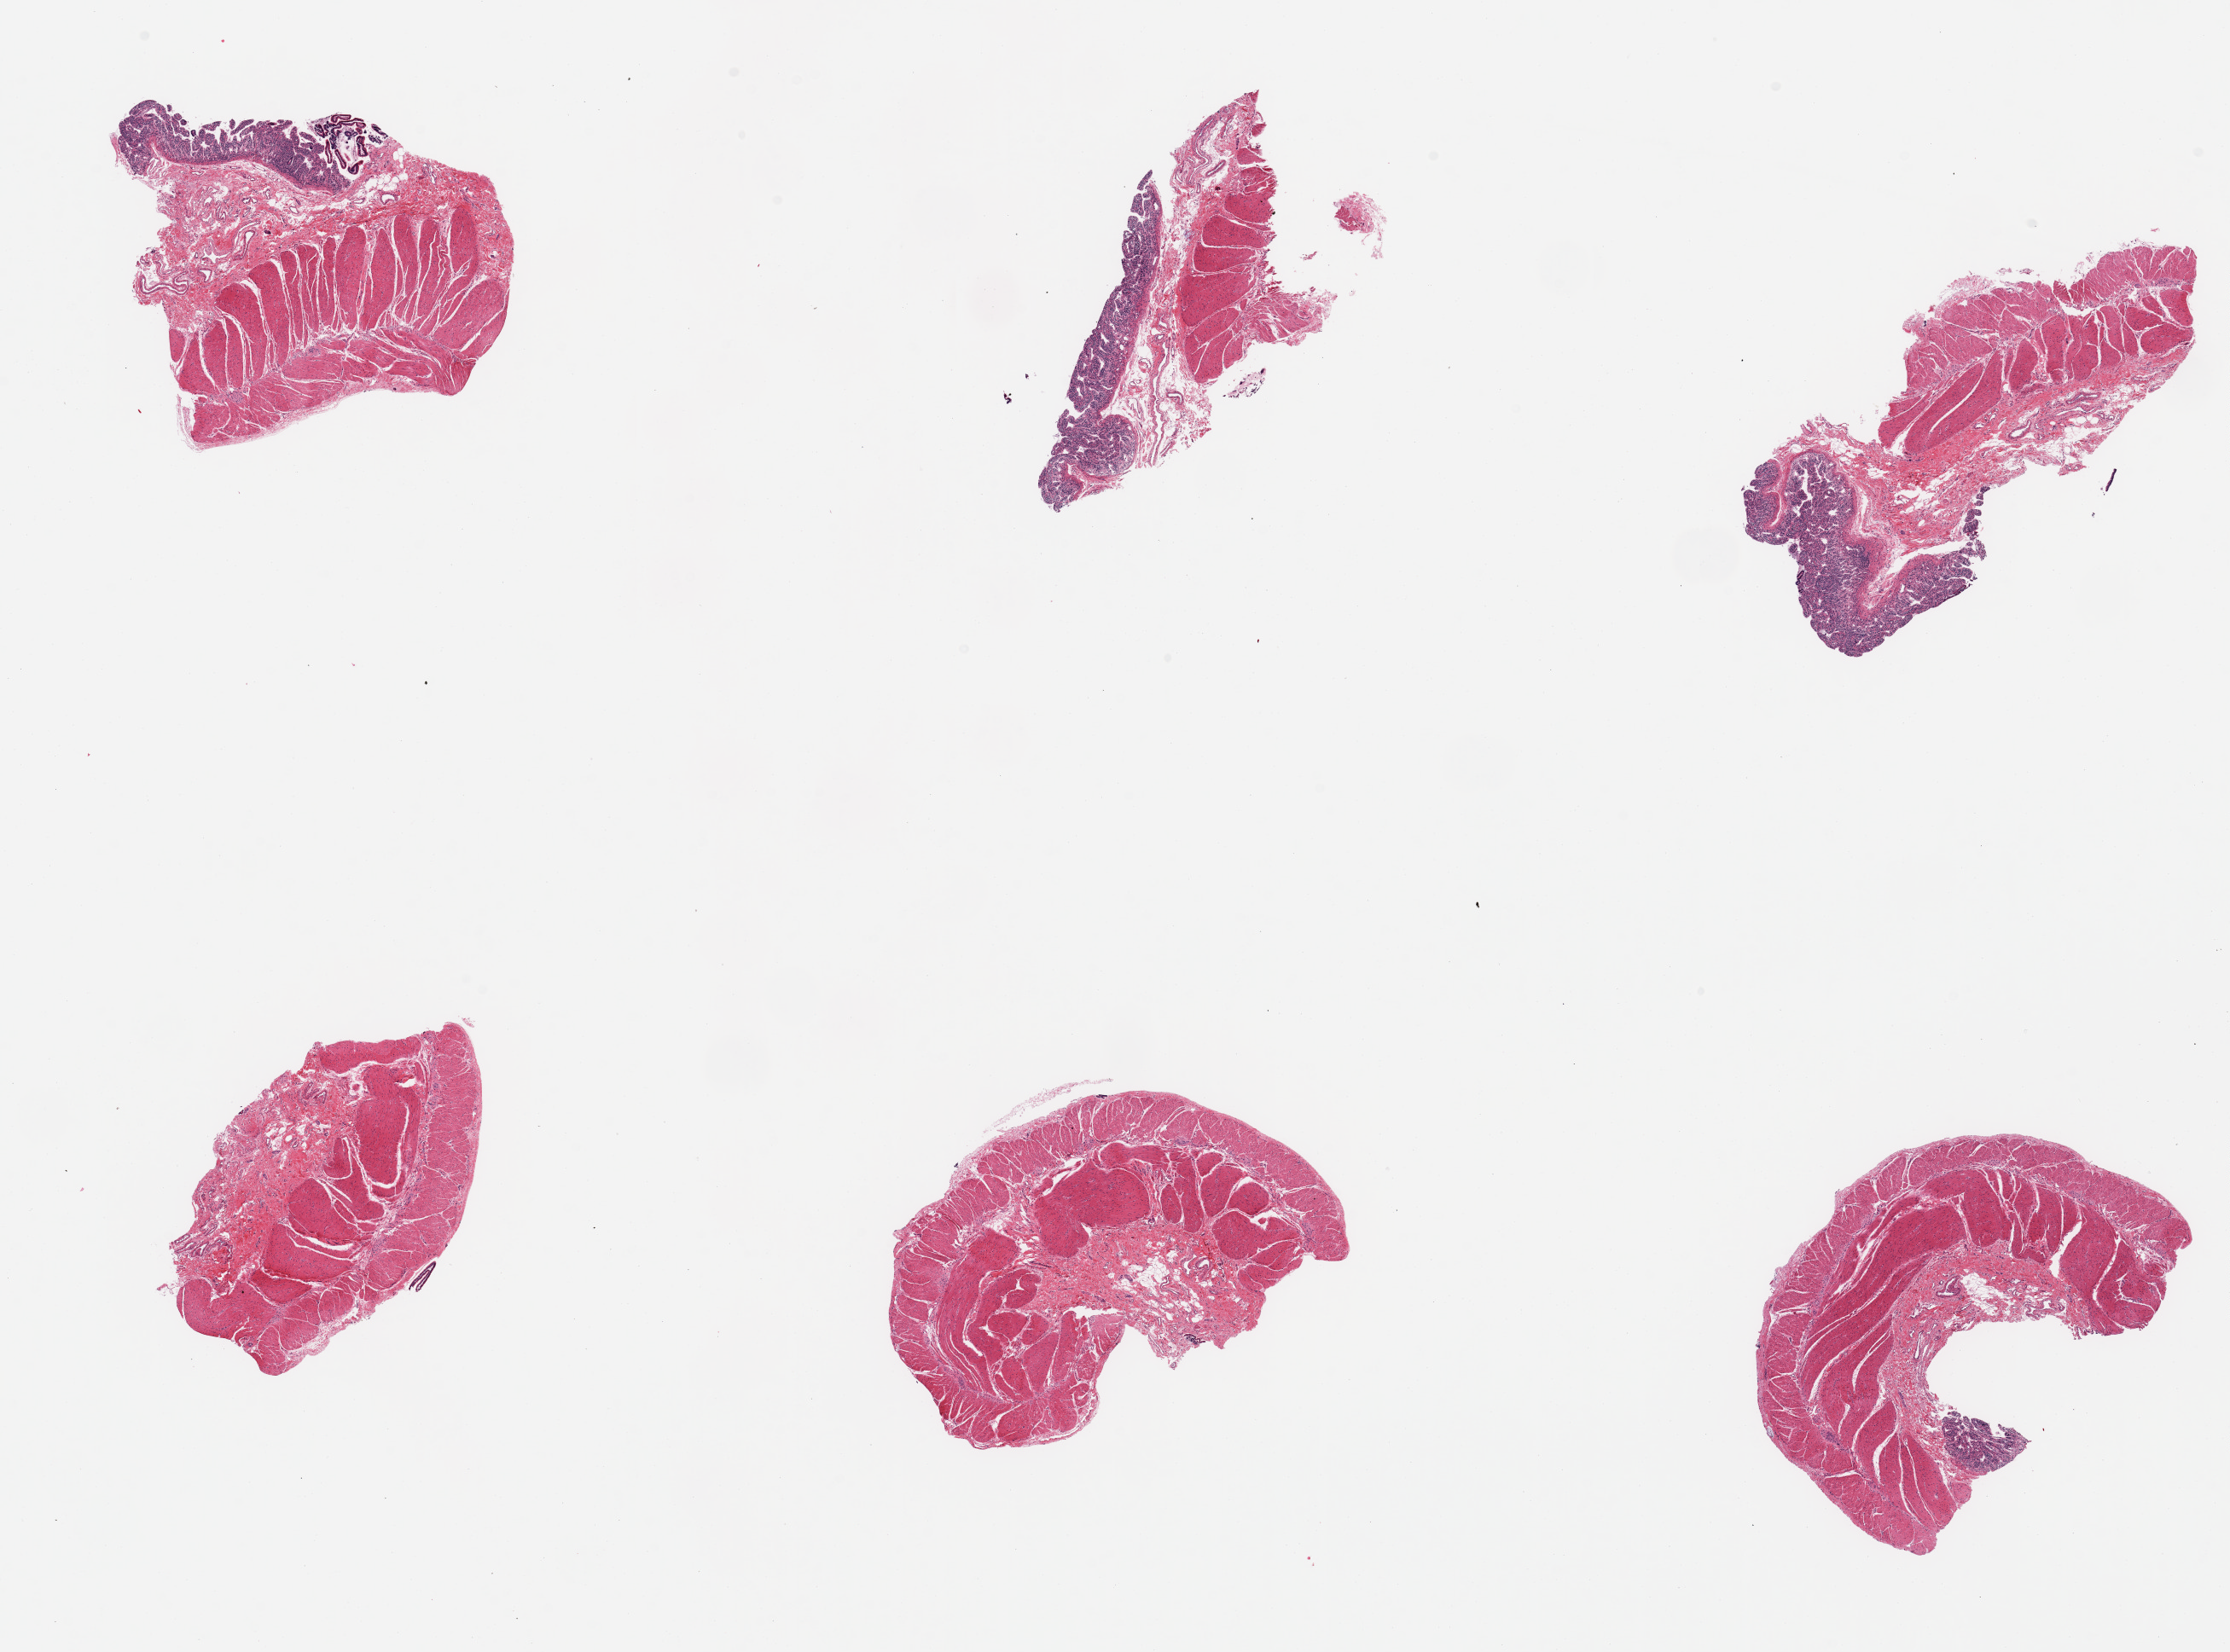
Haematoxylin and eosin whole-slide image, shown as a low-resolution overview of the whole scanned area (about 20.7 x 15.3 mm); PAXgene-fixed paraffin-embedded (PFPE) section; sampled site (target tissue): sigmoid colon; donor tissue sample.
* pathologist's review note for this sample: 6 pieces; mucosa present on most pieces; muscularis on all